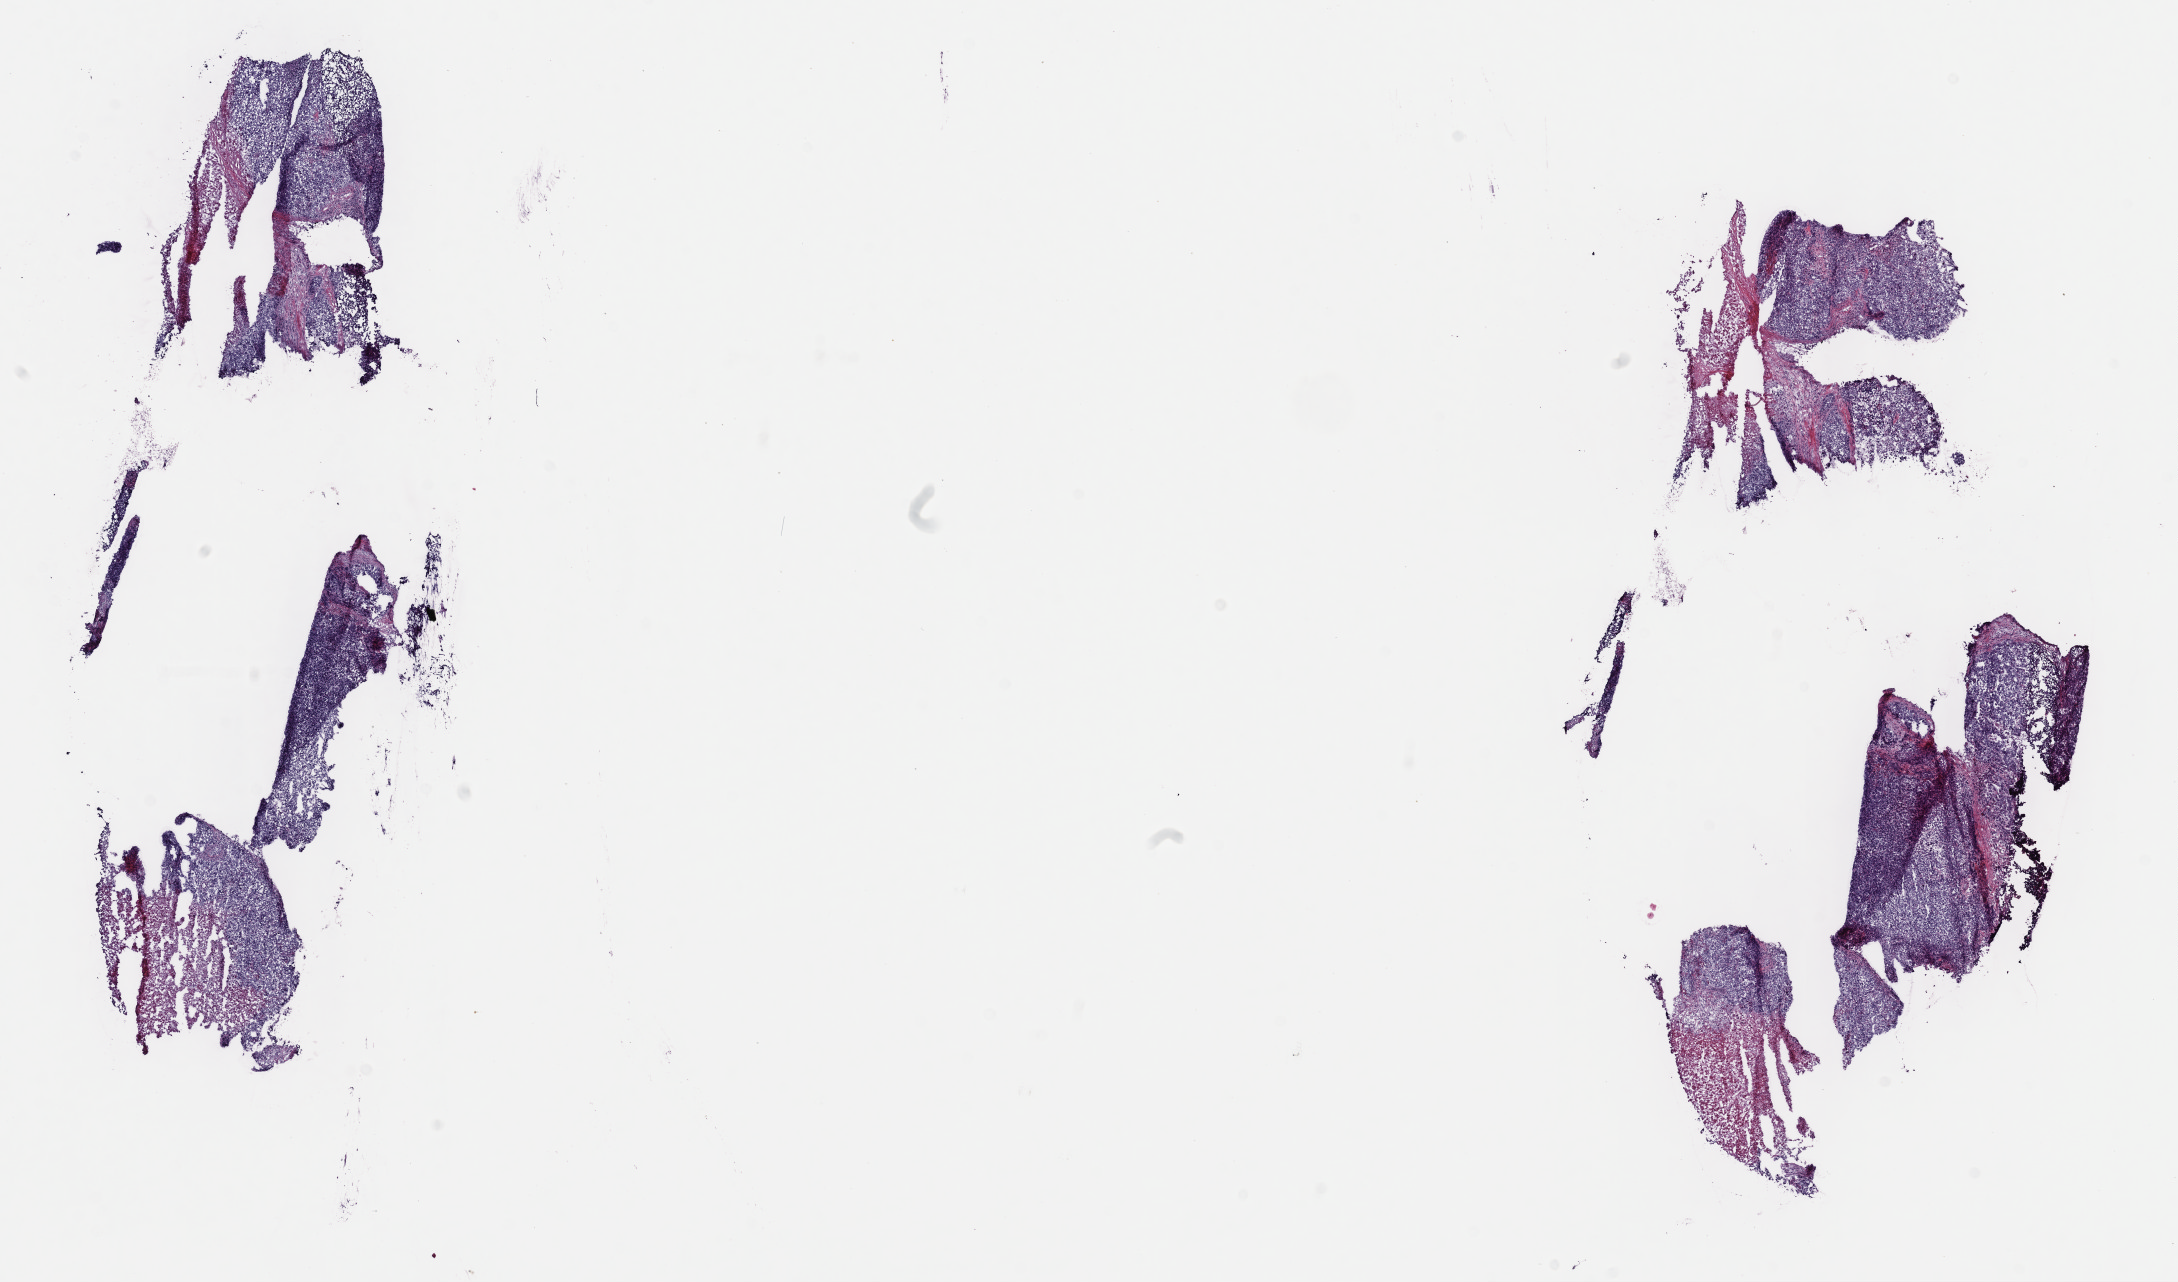
Hematoxylin and eosin (H&E) stained whole-slide image, a low-resolution overview of the entire scanned area, about 17.6 x 10.4 mm (from a 40x scan). Frozen section from the top of the tissue portion. Testis, primary tumour sample. Patient: male, age at initial diagnosis 32 years. Pathologist review of this section (percent, as recorded): tumour cells 85%, tumour nuclei 90%, normal cells 0%, stromal cells 15%, necrosis 0%. Infiltration values recorded for this section: lymphocyte infiltration 0%, monocyte infiltration 0%, neutrophil infiltration 0%.
AJCC pathologic stage: IS. Histologic diagnosis: Embryonal carcinoma, NOS.